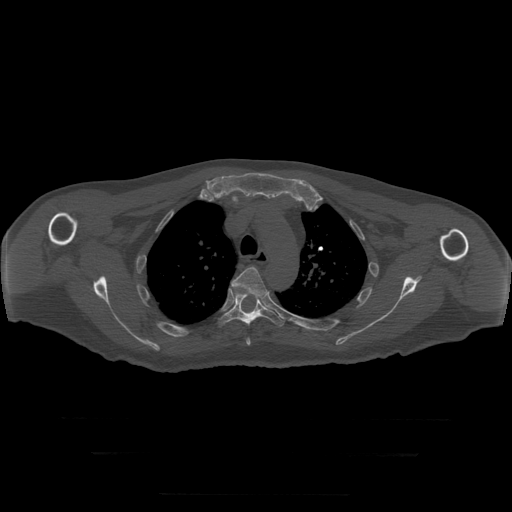
CT including the spine, one axial slice; slice 232 of 397 in the series (ordered by position); reconstruction kernel STANDARD; 120 kVp; bone window (W 1800 / L 400 HU); 1.25 mm slice thickness; 512 × 512 image matrix, field of view 510 × 510 mm. Patient age 73 years. From the clinical record (not read from this slice): primary cancer: prostate.
Structures marked on this image (semi-automatically segmented with operator editing):
- T4 vertebra: bounding box (x1, y1, x2, y2) in pixels: (231, 267, 267, 346)
- T5 vertebra: (218, 288, 285, 328)